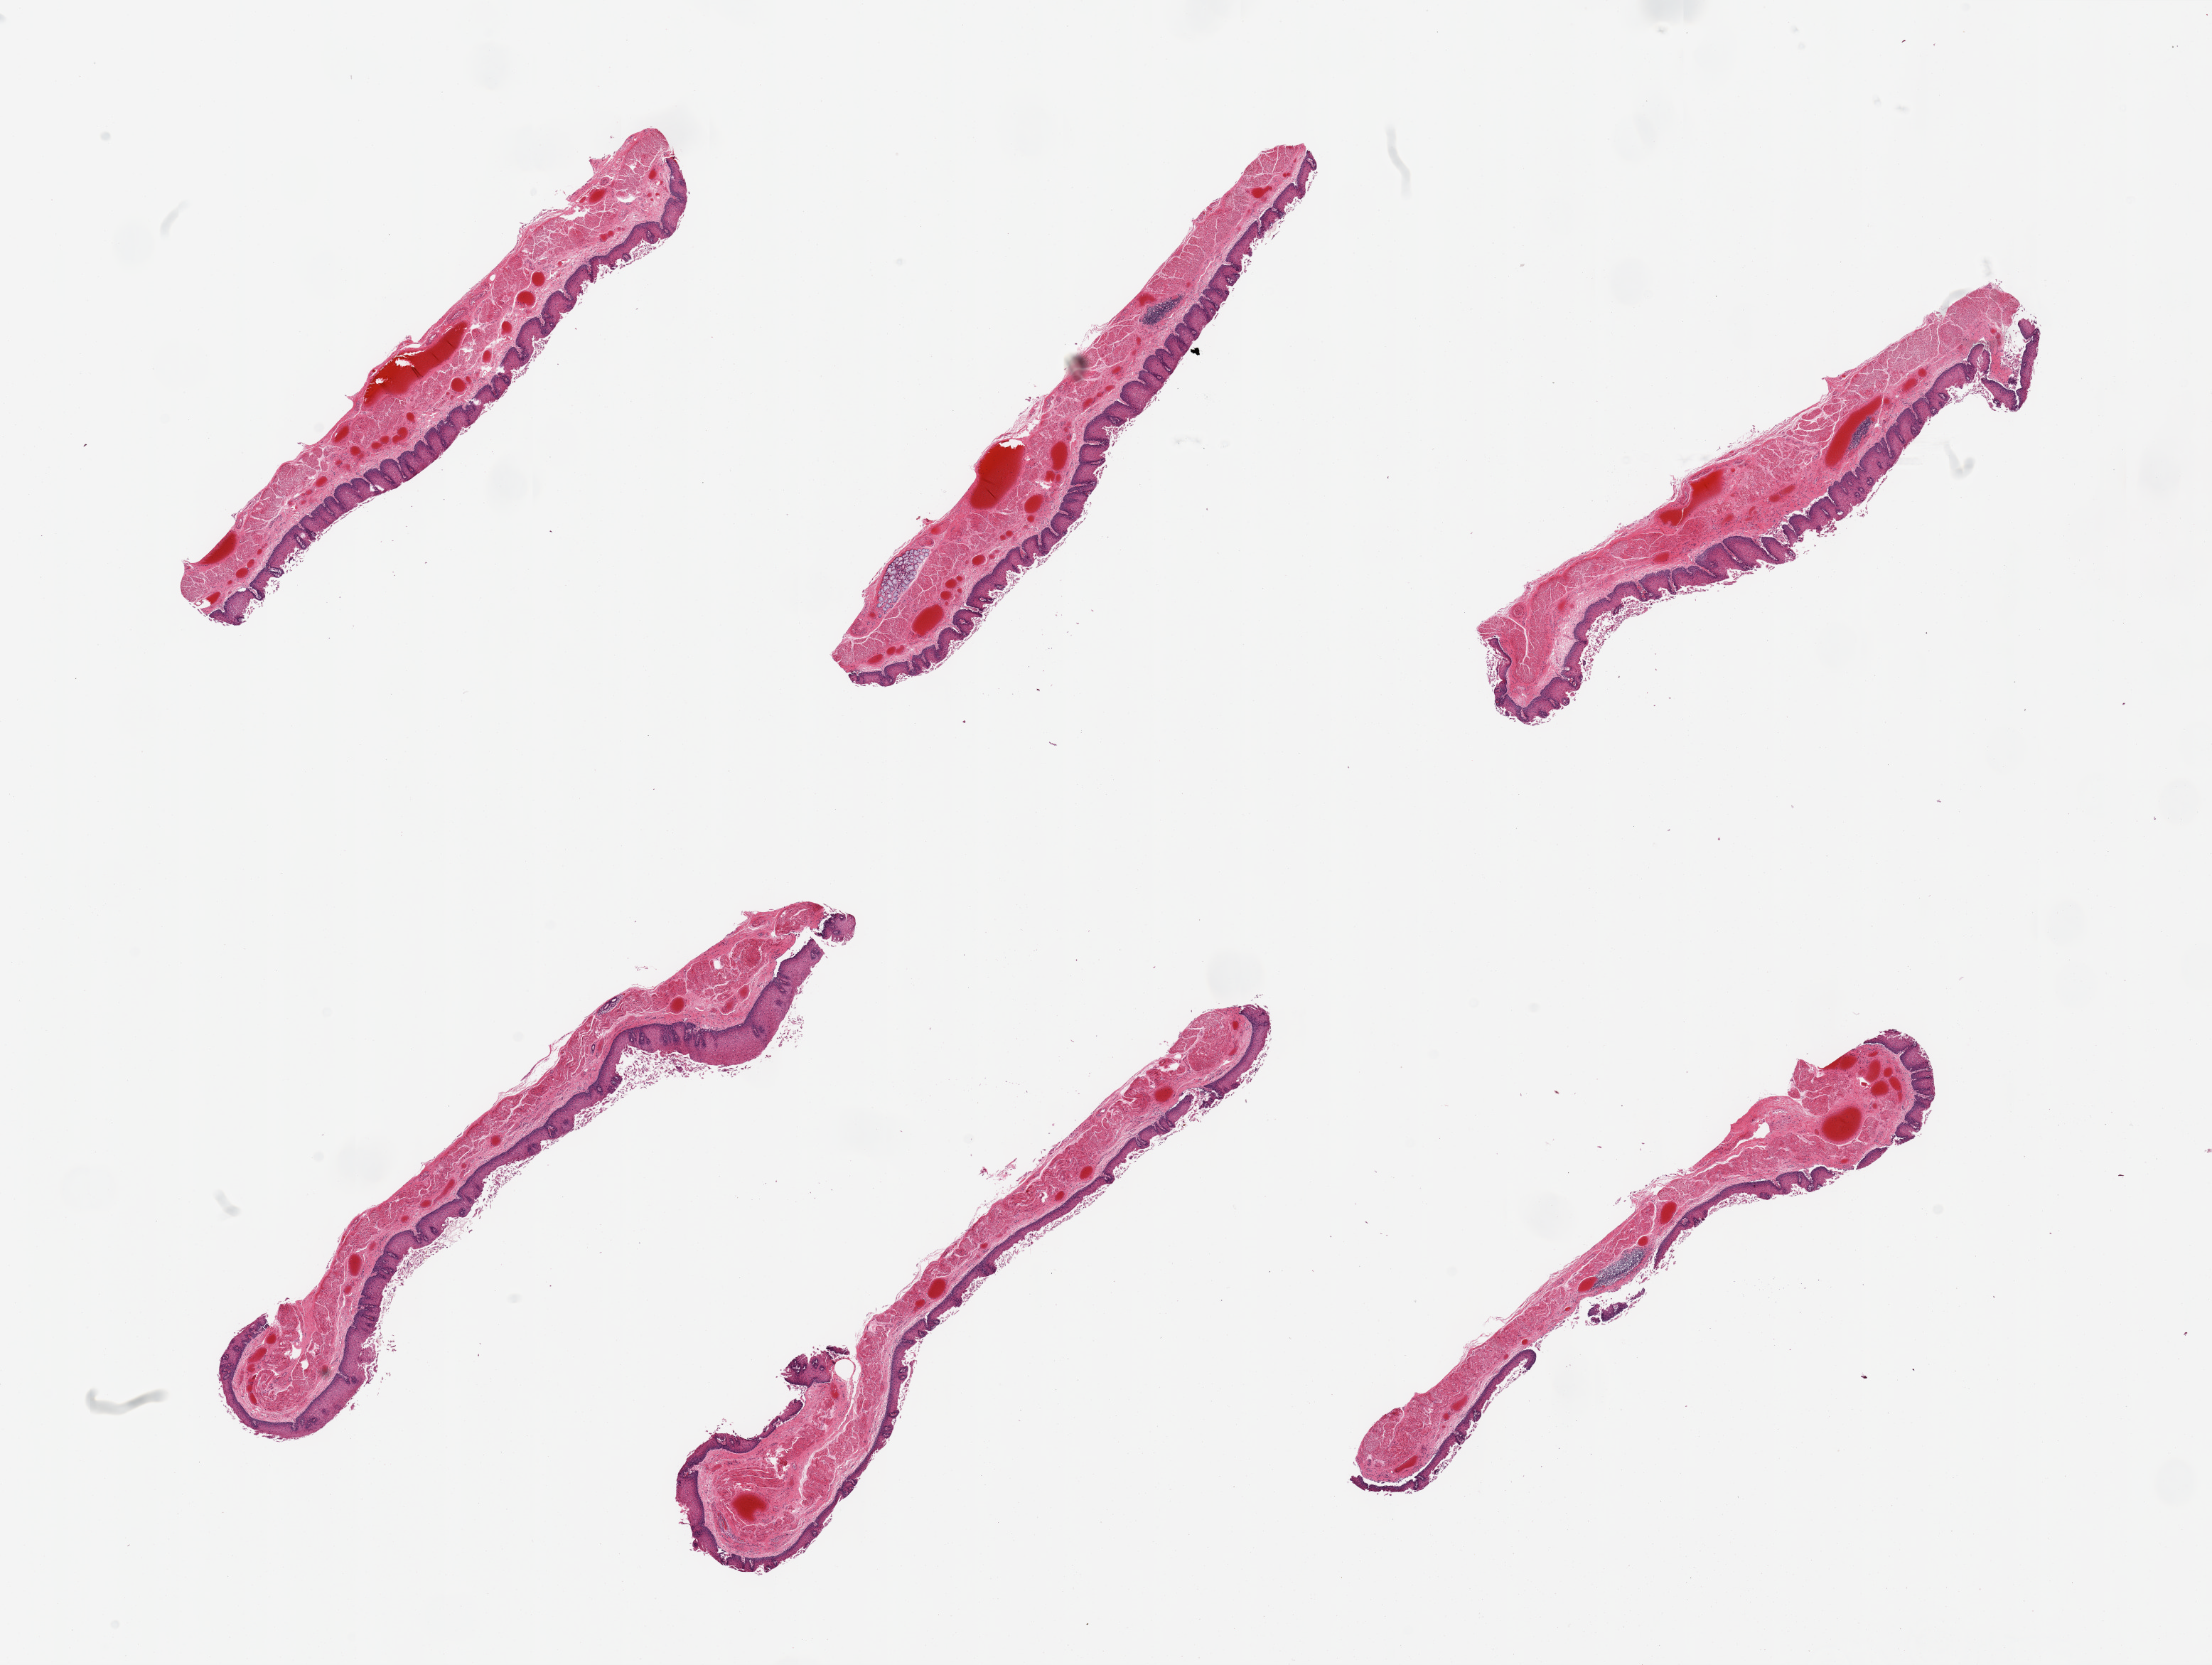
H&E whole-slide image, low-resolution overview of the scanned area, about 24.6 x 18.5 mm (slide scanned at 20x); PAXgene-fixed paraffin-embedded (PFPE) section; target tissue: esophageal mucous membrane; donor tissue sample.
• reviewer comment on this tissue sample: 6 pieces; well dissected; partial epithelial sloughing